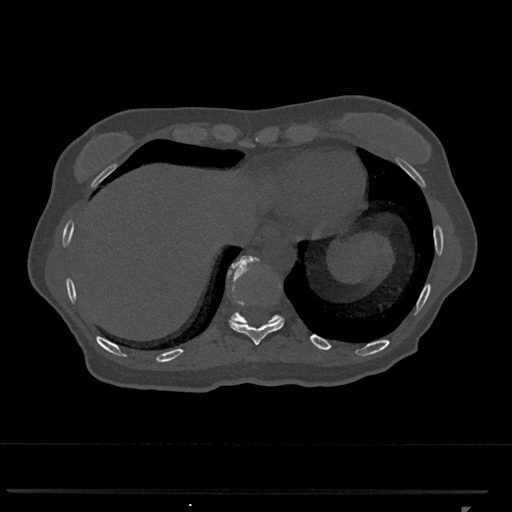
CT including the spine, one axial slice. Reconstruction kernel Br40s/3. 120 kVp. Bone window (W 1800 / L 400 HU). 512 × 512 image matrix. Patient: female, 62 years. From the clinical record (not read from this slice): primary cancer: renal.
Annotated regions visible in this slice (semi-automatically segmented with operator editing):
- T10 vertebra: bounding box (x1, y1, x2, y2) in pixels: (229, 266, 285, 346)
- T11 vertebra: (227, 255, 282, 325)